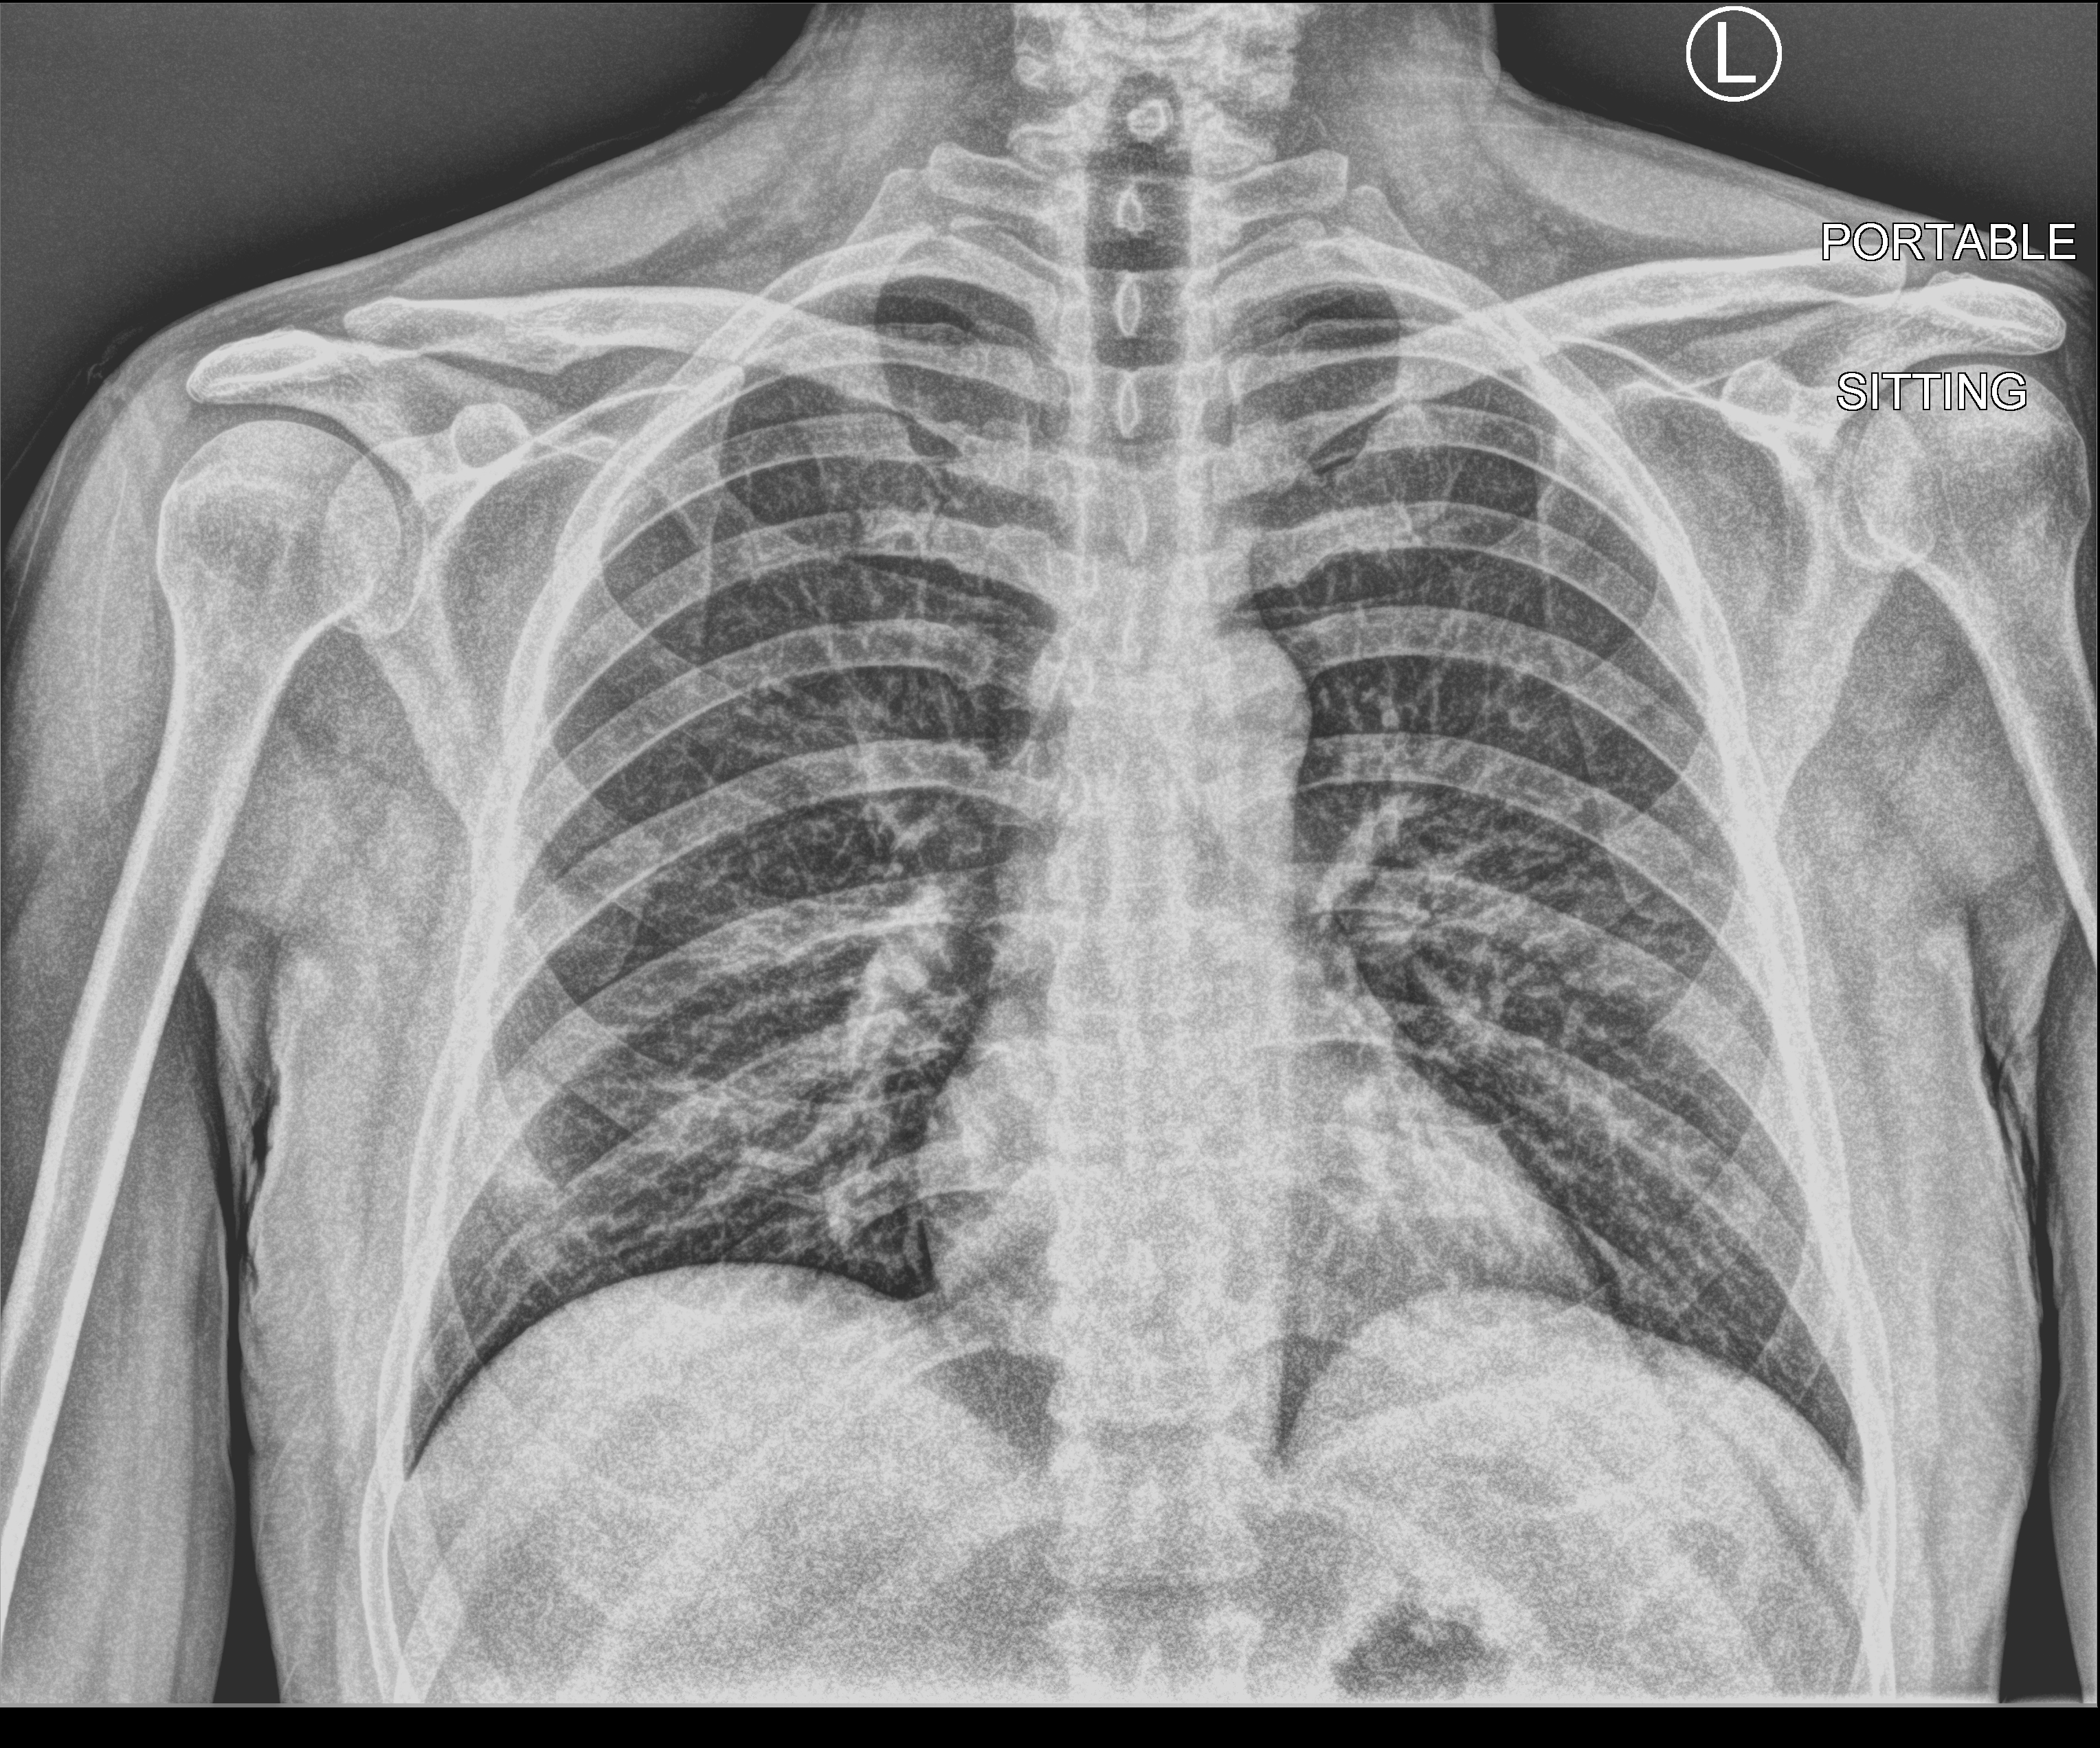
Bedside chest radiograph (computed radiography). Patient hospitalised with COVID-19; male, aged 18–59 years.
From the hospital-stay record, not from the radiograph (when in the stay this image was taken is not recorded):
- admitted to intensive care during this hospital stay: no
- chronic kidney disease (admission record): no
- mechanically ventilated during this hospital stay: no